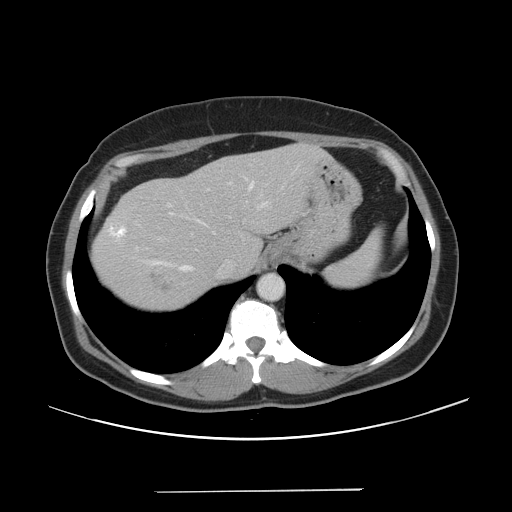
Contrast-enhanced abdominal CT, one axial slice; slice 37 of 56 in the series (ordered by position); intravenous contrast given; soft-tissue window (W 400 / L 40 HU); 512 × 512 image matrix. Female patient, age 54 years. Case-level facts recorded for this patient, not image findings: diagnosis: colorectal cancer liver metastases, imaged before liver resection; multiple liver metastases: yes; largest metastasis: 3.2 cm; chemotherapy before resection: yes.
Outlined on this slice (expert manual segmentation):
- hepatic veins: bounding box [x1, y1, x2, y2] px = [131, 177, 269, 272]
- liver: [92, 144, 326, 313]
- planned liver remnant (the part of the liver to remain after resection): [193, 143, 326, 273]
- portal vein (with intrahepatic branches): [206, 181, 233, 191]
- liver metastasis: [151, 266, 172, 290]
- liver metastasis: [108, 218, 128, 240]